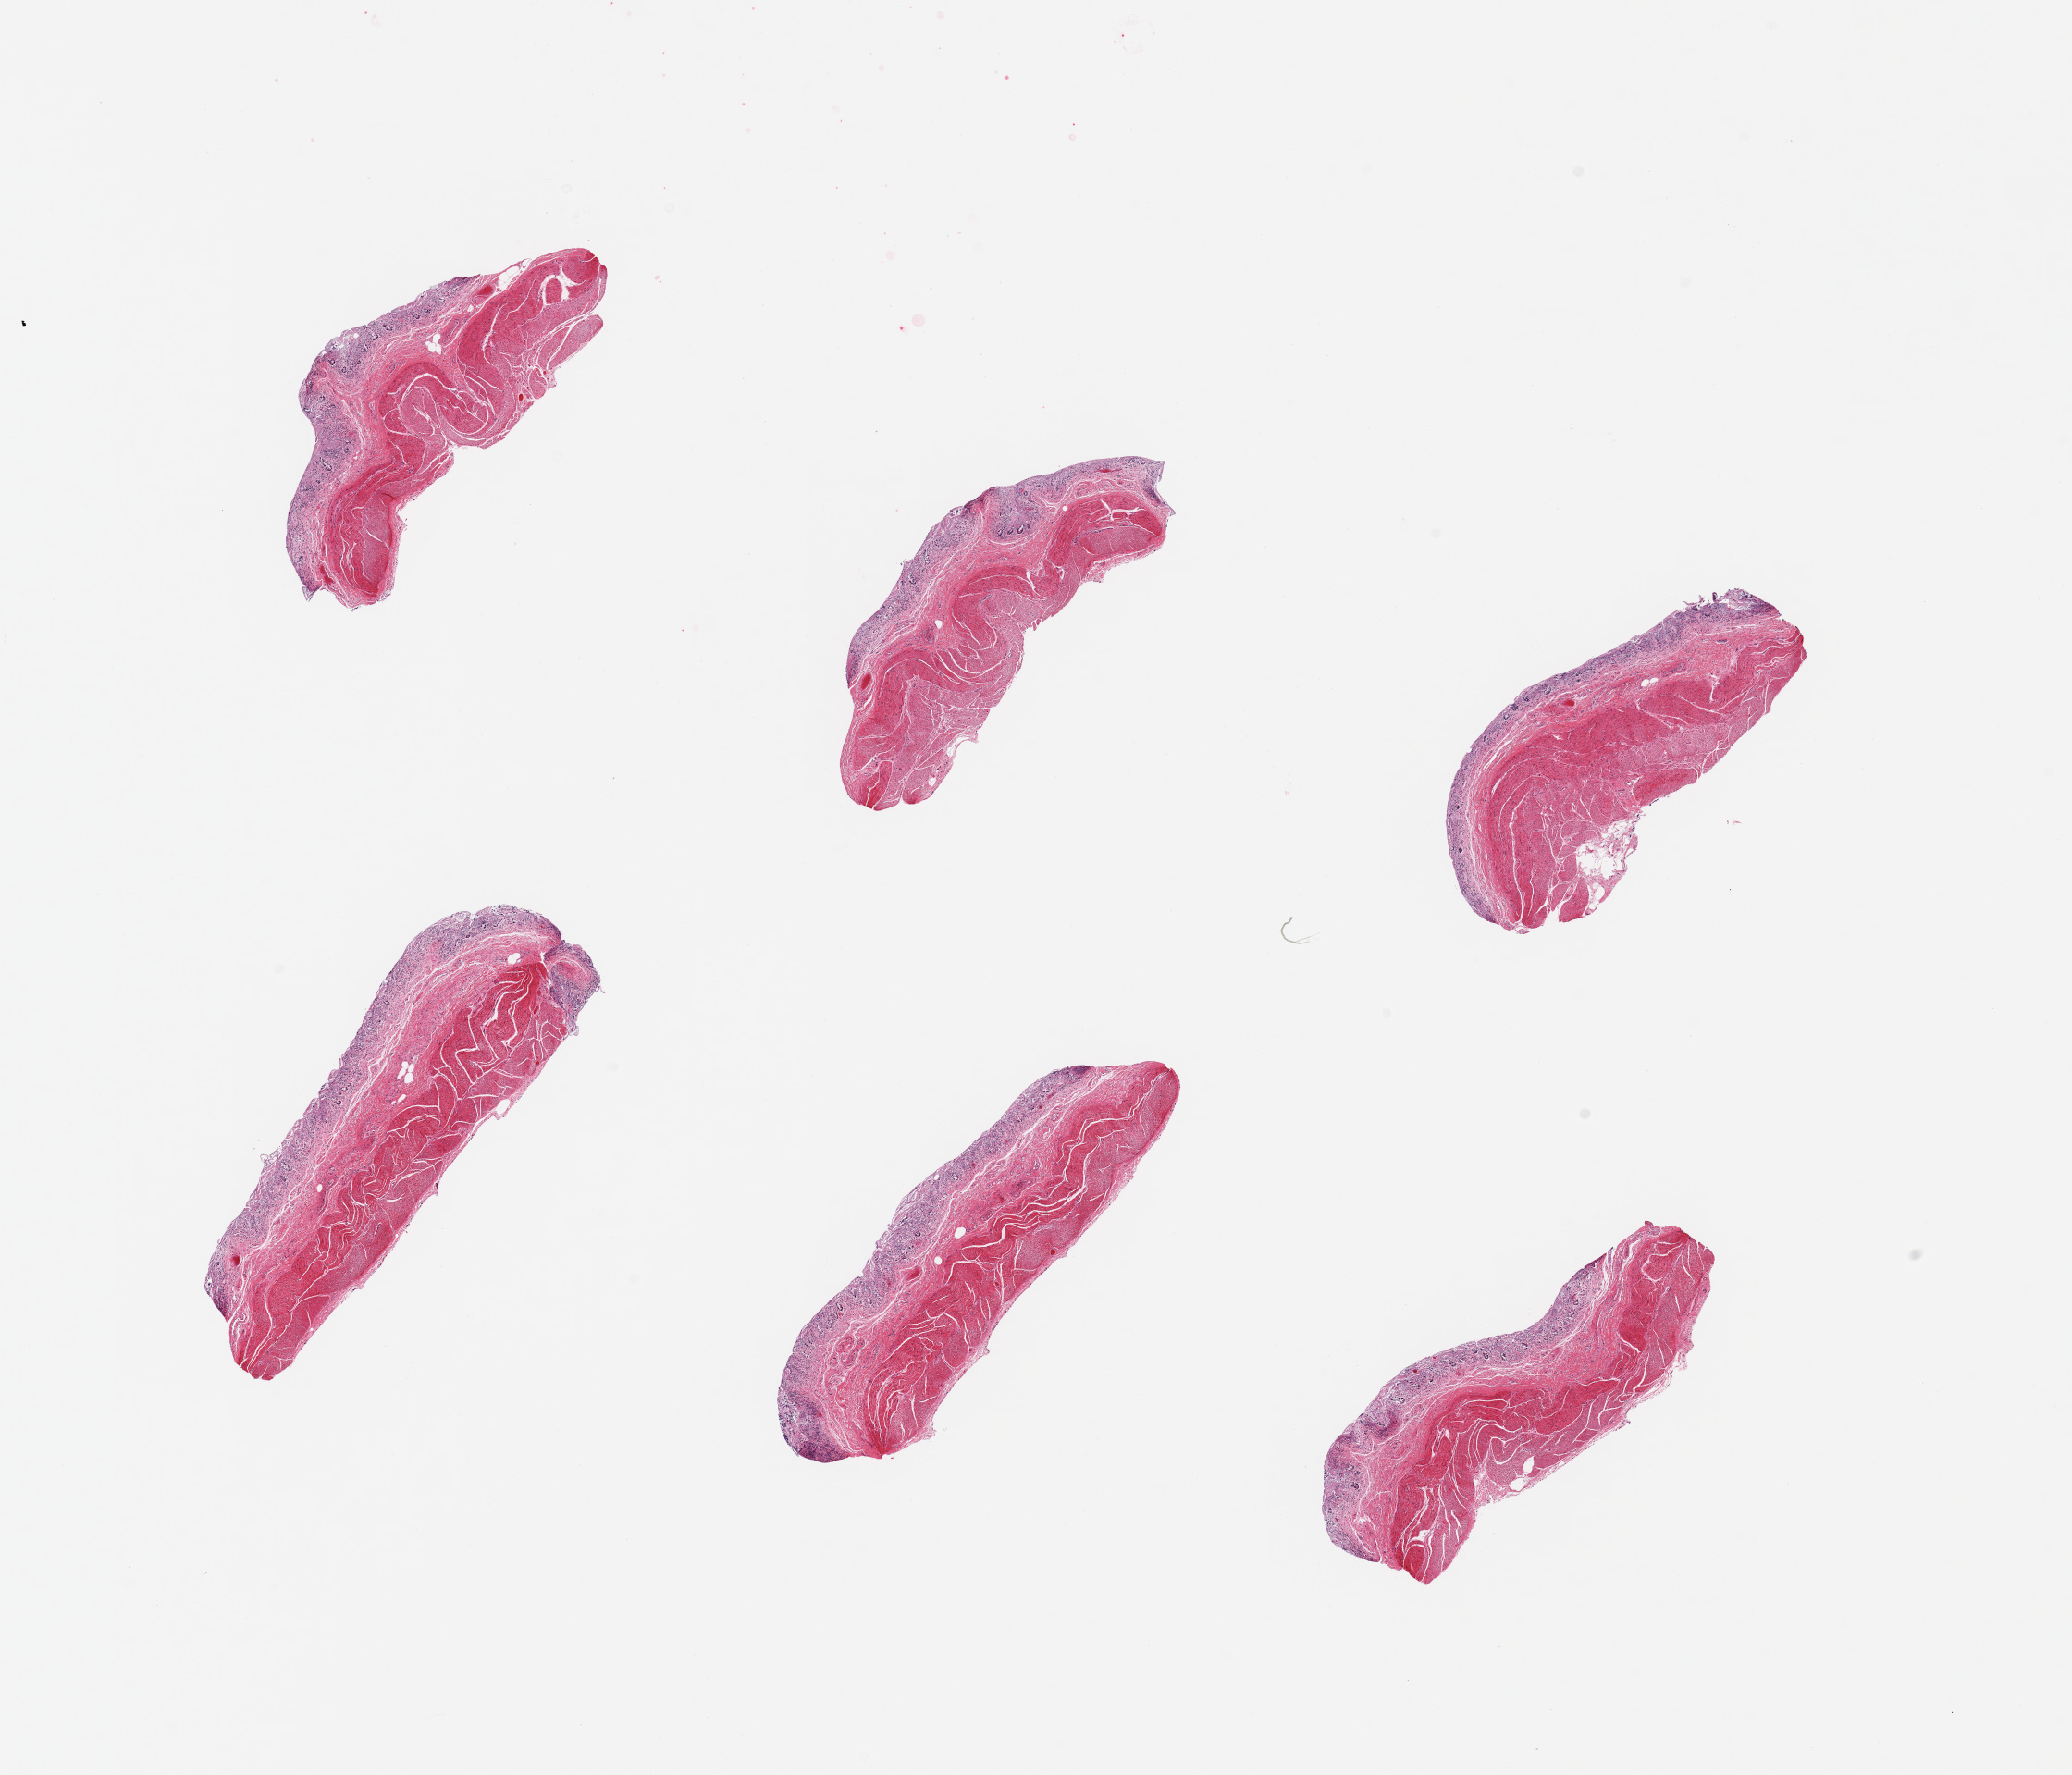
Whole-slide image, haematoxylin and eosin stain, whole scanned area (about 17.7 x 15.2 mm) shown as a low-resolution overview, PAXgene-fixed paraffin-embedded (PFPE) section, target tissue: ileum, tissue donor sample. Donor sex: female.
* review note (as recorded): 6 pieces; mucosa totally autolyzed; no lymphoid collections; muscularis in all; (resembles colon)